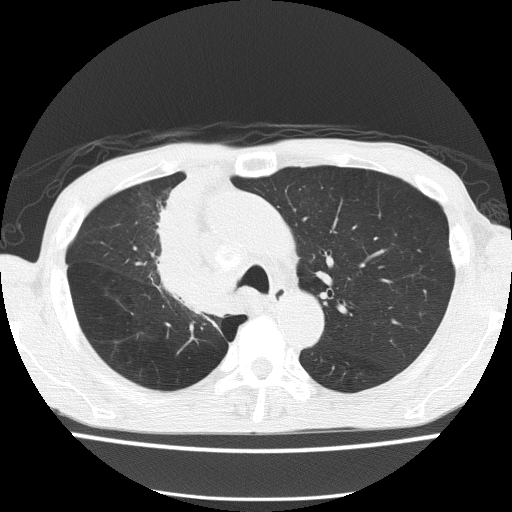
Low-dose screening chest CT, one axial slice; position 104 of 150 along the scan axis; reconstruction kernel FC51; 120 kVp; lung window (W 1500 / L -600 HU); 512 × 512 image matrix.
Structures marked on this image (outlined manually by an expert reader):
- lesion 1 (tumor, hilum of right lung): bounding box (x1, y1, x2, y2) in pixels: (161, 178, 230, 317)